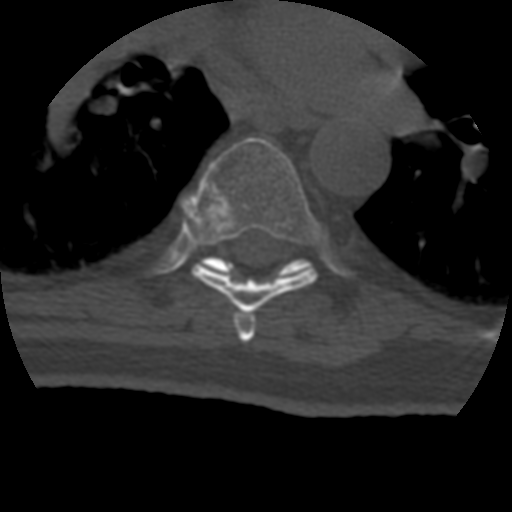
CT including the spine, one axial slice. Slice 276 of 399 in the series (ordered by position). Reconstruction kernel STANDARD. 120 kVp. Bone window (W 1800 / L 400 HU). 1.25 mm slice thickness. 512 × 512 image matrix, field of view 160 × 160 mm. Patient age 69 years. From the clinical record (not read from this slice): primary cancer: prostate.
Outlined on this slice (semi-automatic segmentation, software-assisted and operator-edited):
- T6 vertebra: box from (x=233, y=312) to (x=256, y=343) px
- T7 vertebra: (x=182, y=137)–(x=322, y=314)
- T8 vertebra: (x=201, y=256)–(x=311, y=276)